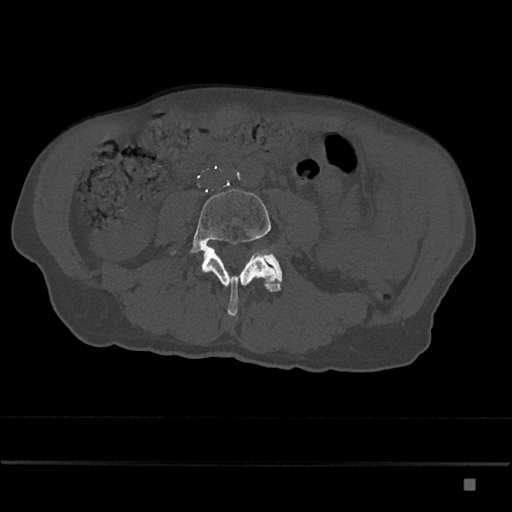
CT including the spine, one axial slice. Slice 331 of 797 in the series (ordered by position). Reconstruction kernel Br40s/3. 120 kVp. Bone window (W 1800 / L 400 HU). 0.5 mm slice thickness. 512 × 512 image matrix, field of view 390 × 390 mm. Patient: male, 72 years. From the clinical record (not read from this slice): primary cancer: prostate.
Structures marked on this image (semi-automatic segmentation, software-assisted and operator-edited):
- L4 vertebra: bounding box (x1, y1, x2, y2) in pixels: (170, 189, 281, 316)
- L5 vertebra: (265, 255, 283, 281)